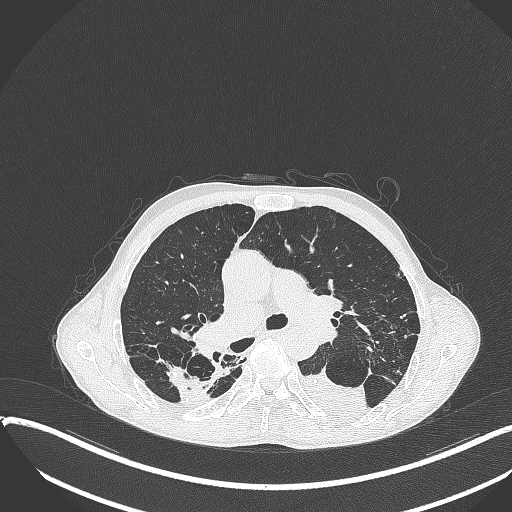
Chest CT, one axial slice. Slice 241 of 401 in the series (ordered by position). Reconstruction kernel B70f. 120 kVp. Lung window (W 1500 / L -600 HU). 512 × 512 image matrix, field of view 400 × 400 mm. Patient: male, 57 years. From the clinical record (not read from this slice): clinical TNM (as recorded): T4 N0 M0.
Structures marked on this image (bounding box drawn by a radiologist):
- lung tumour (recorded histology: squamous cell carcinoma): bounding box <301,368,373,421> (left, top, right, bottom; pixels)